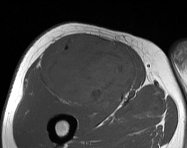
MRI of an extremity soft-tissue mass, one axial slice. Slice 89 of 114 in the series (ordered by position). MR volume resampled by the dataset authors to the PET/CT grid (not the native acquisition matrix). 187 × 148 image matrix, field of view 183 × 145 mm. Male patient. From the clinical record (not read from this slice): histological type: pleiomorphic leiomyosarcoma; grade: intermediate; site of the primary tumour: right thigh.
Annotated regions visible in this slice (expert contour drawn on MRI and transferred to this co-registered scan by the dataset authors):
- gross tumour volume including surrounding oedema: box from (x=43, y=36) to (x=135, y=105) px
- gross tumour volume (mass): (x=43, y=36)–(x=135, y=105)